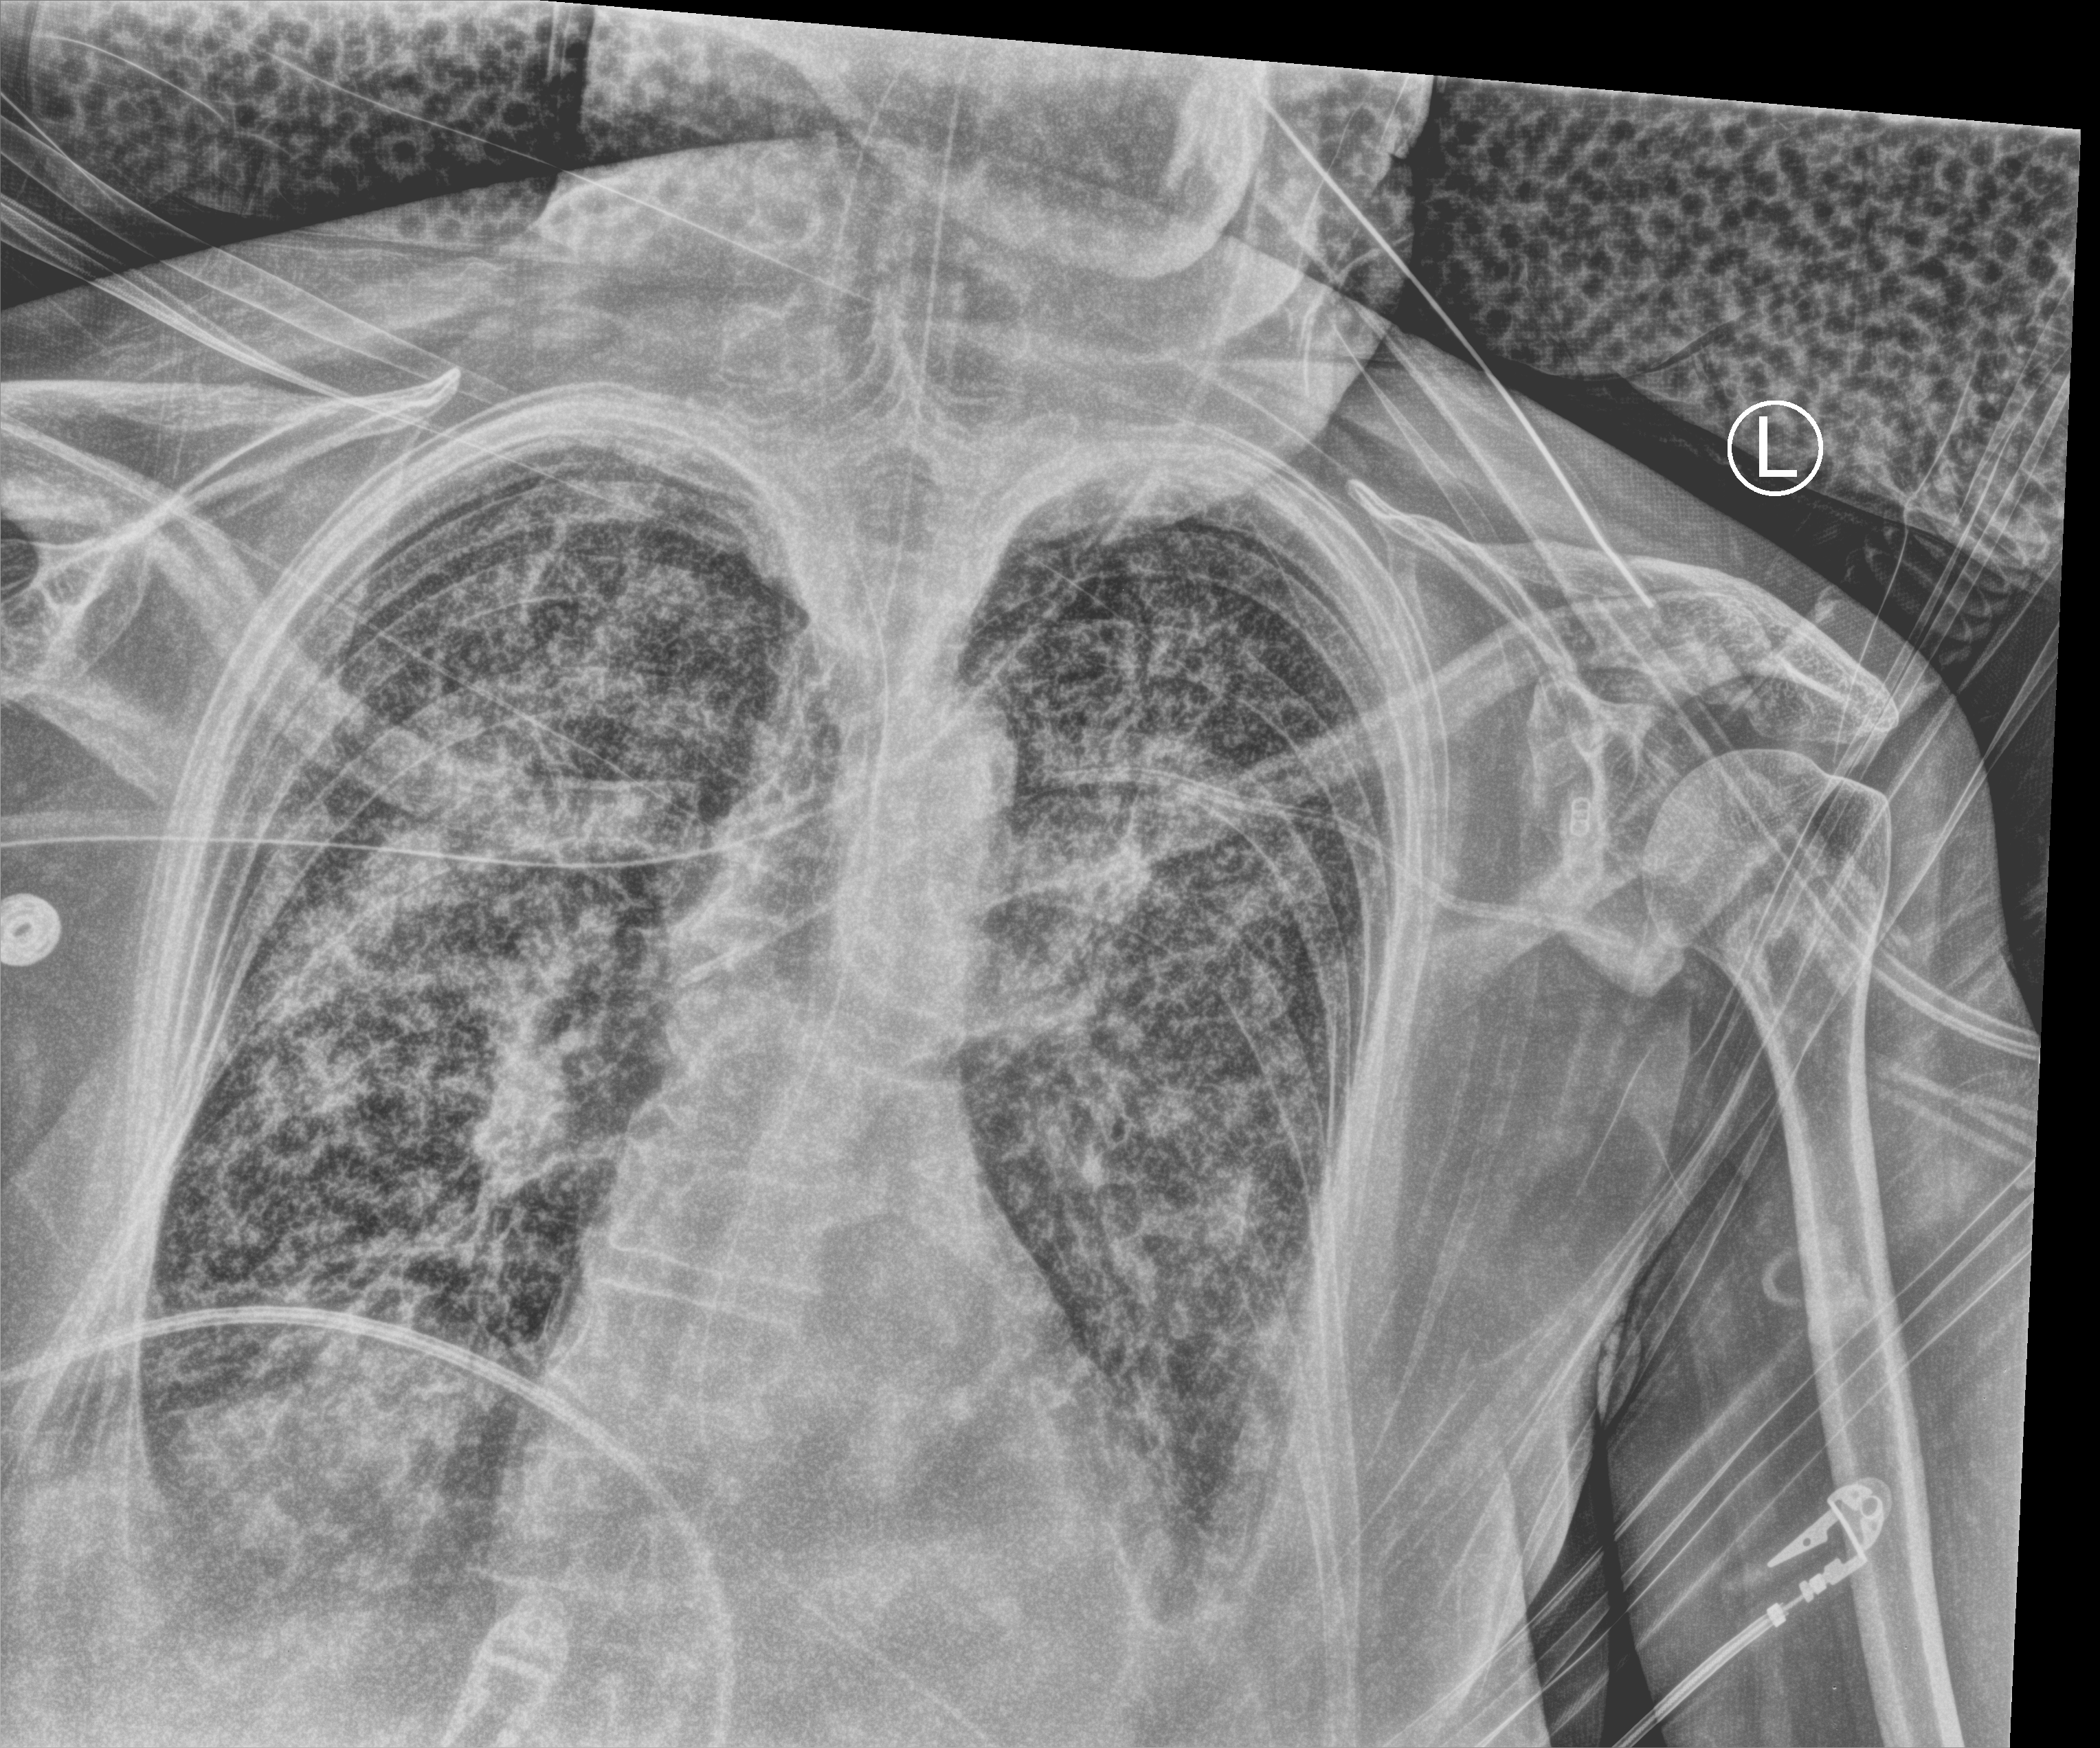
Portable chest radiograph. Female patient hospitalised with COVID-19, age 75–90 years.
Hospital-stay facts (about this admission, not read from this image; timing relative to this image not recorded): mechanically ventilated during this hospital stay: yes.